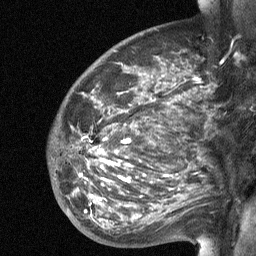
Breast MRI (dynamic contrast-enhanced), one sagittal slice; dynamic contrast-enhanced study with each time point stored as its own series, time point 2 of 3 at this slice position (early post-contrast, ordered by acquisition time); 1.5 T; TE 4.8 ms, TR 27 ms; 2 mm slice thickness; 256 × 256 image matrix, field of view 200 × 200 mm. Patient: female, 50 years. From the clinical record (not read from this slice): setting: breast cancer imaged before/during neoadjuvant chemotherapy; receptor status: HER2-positive.
Outlined on this slice (semi-automatically segmented with operator editing):
- analysis volume of interest (the breast-tissue region the enhancement analysis was run in; not a lesion): box from (x=53, y=91) to (x=204, y=227) px
- tumour enhancement mask (voxels above the 90 % enhancement threshold inside the analysis volume of interest): (x=98, y=150)–(x=130, y=181)